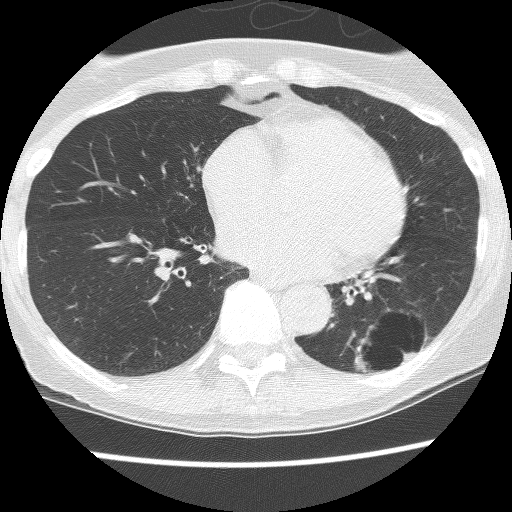
Axial slice from a low-dose chest CT screening exam. Third screening round (two years after baseline). Lung window (W 1500 / L -600 HU). 120 kVp. 512 × 512 image matrix. Female participant, aged 61 years at enrolment.
Lesion marked by an expert reader, bounding box (x1, y1, x2, y2) in pixels: (329, 289, 450, 391). The screening reader recorded 2 non-calcified nodules or masses ≥4 mm on this exam (left lower lobe, left lower lobe); which of them this box marks is not recorded. Official screen result: positive, no significant change: stable abnormalities potentially related to lung cancer, unchanged since the prior screening exam.